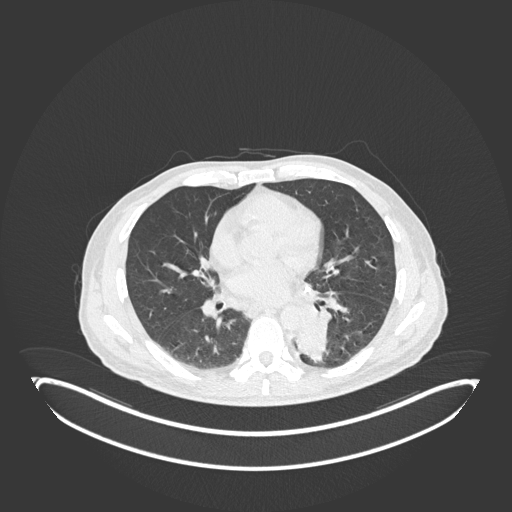
Chest CT, one axial slice; slice 89 of 251 in the series (ordered by position); reconstruction kernel B30f; lung window (W 1500 / L -600 HU); 1 mm slice thickness; 512 × 512 image matrix. Patient: male, 72 years. Case-level facts recorded for this patient, not image findings: clinical TNM (as recorded): T2b N0 M1.
Outlined on this slice (bounding box drawn by a radiologist):
- lung tumour (recorded histology: adenocarcinoma): bounding box (x1, y1, x2, y2) in pixels: (290, 318, 331, 367)